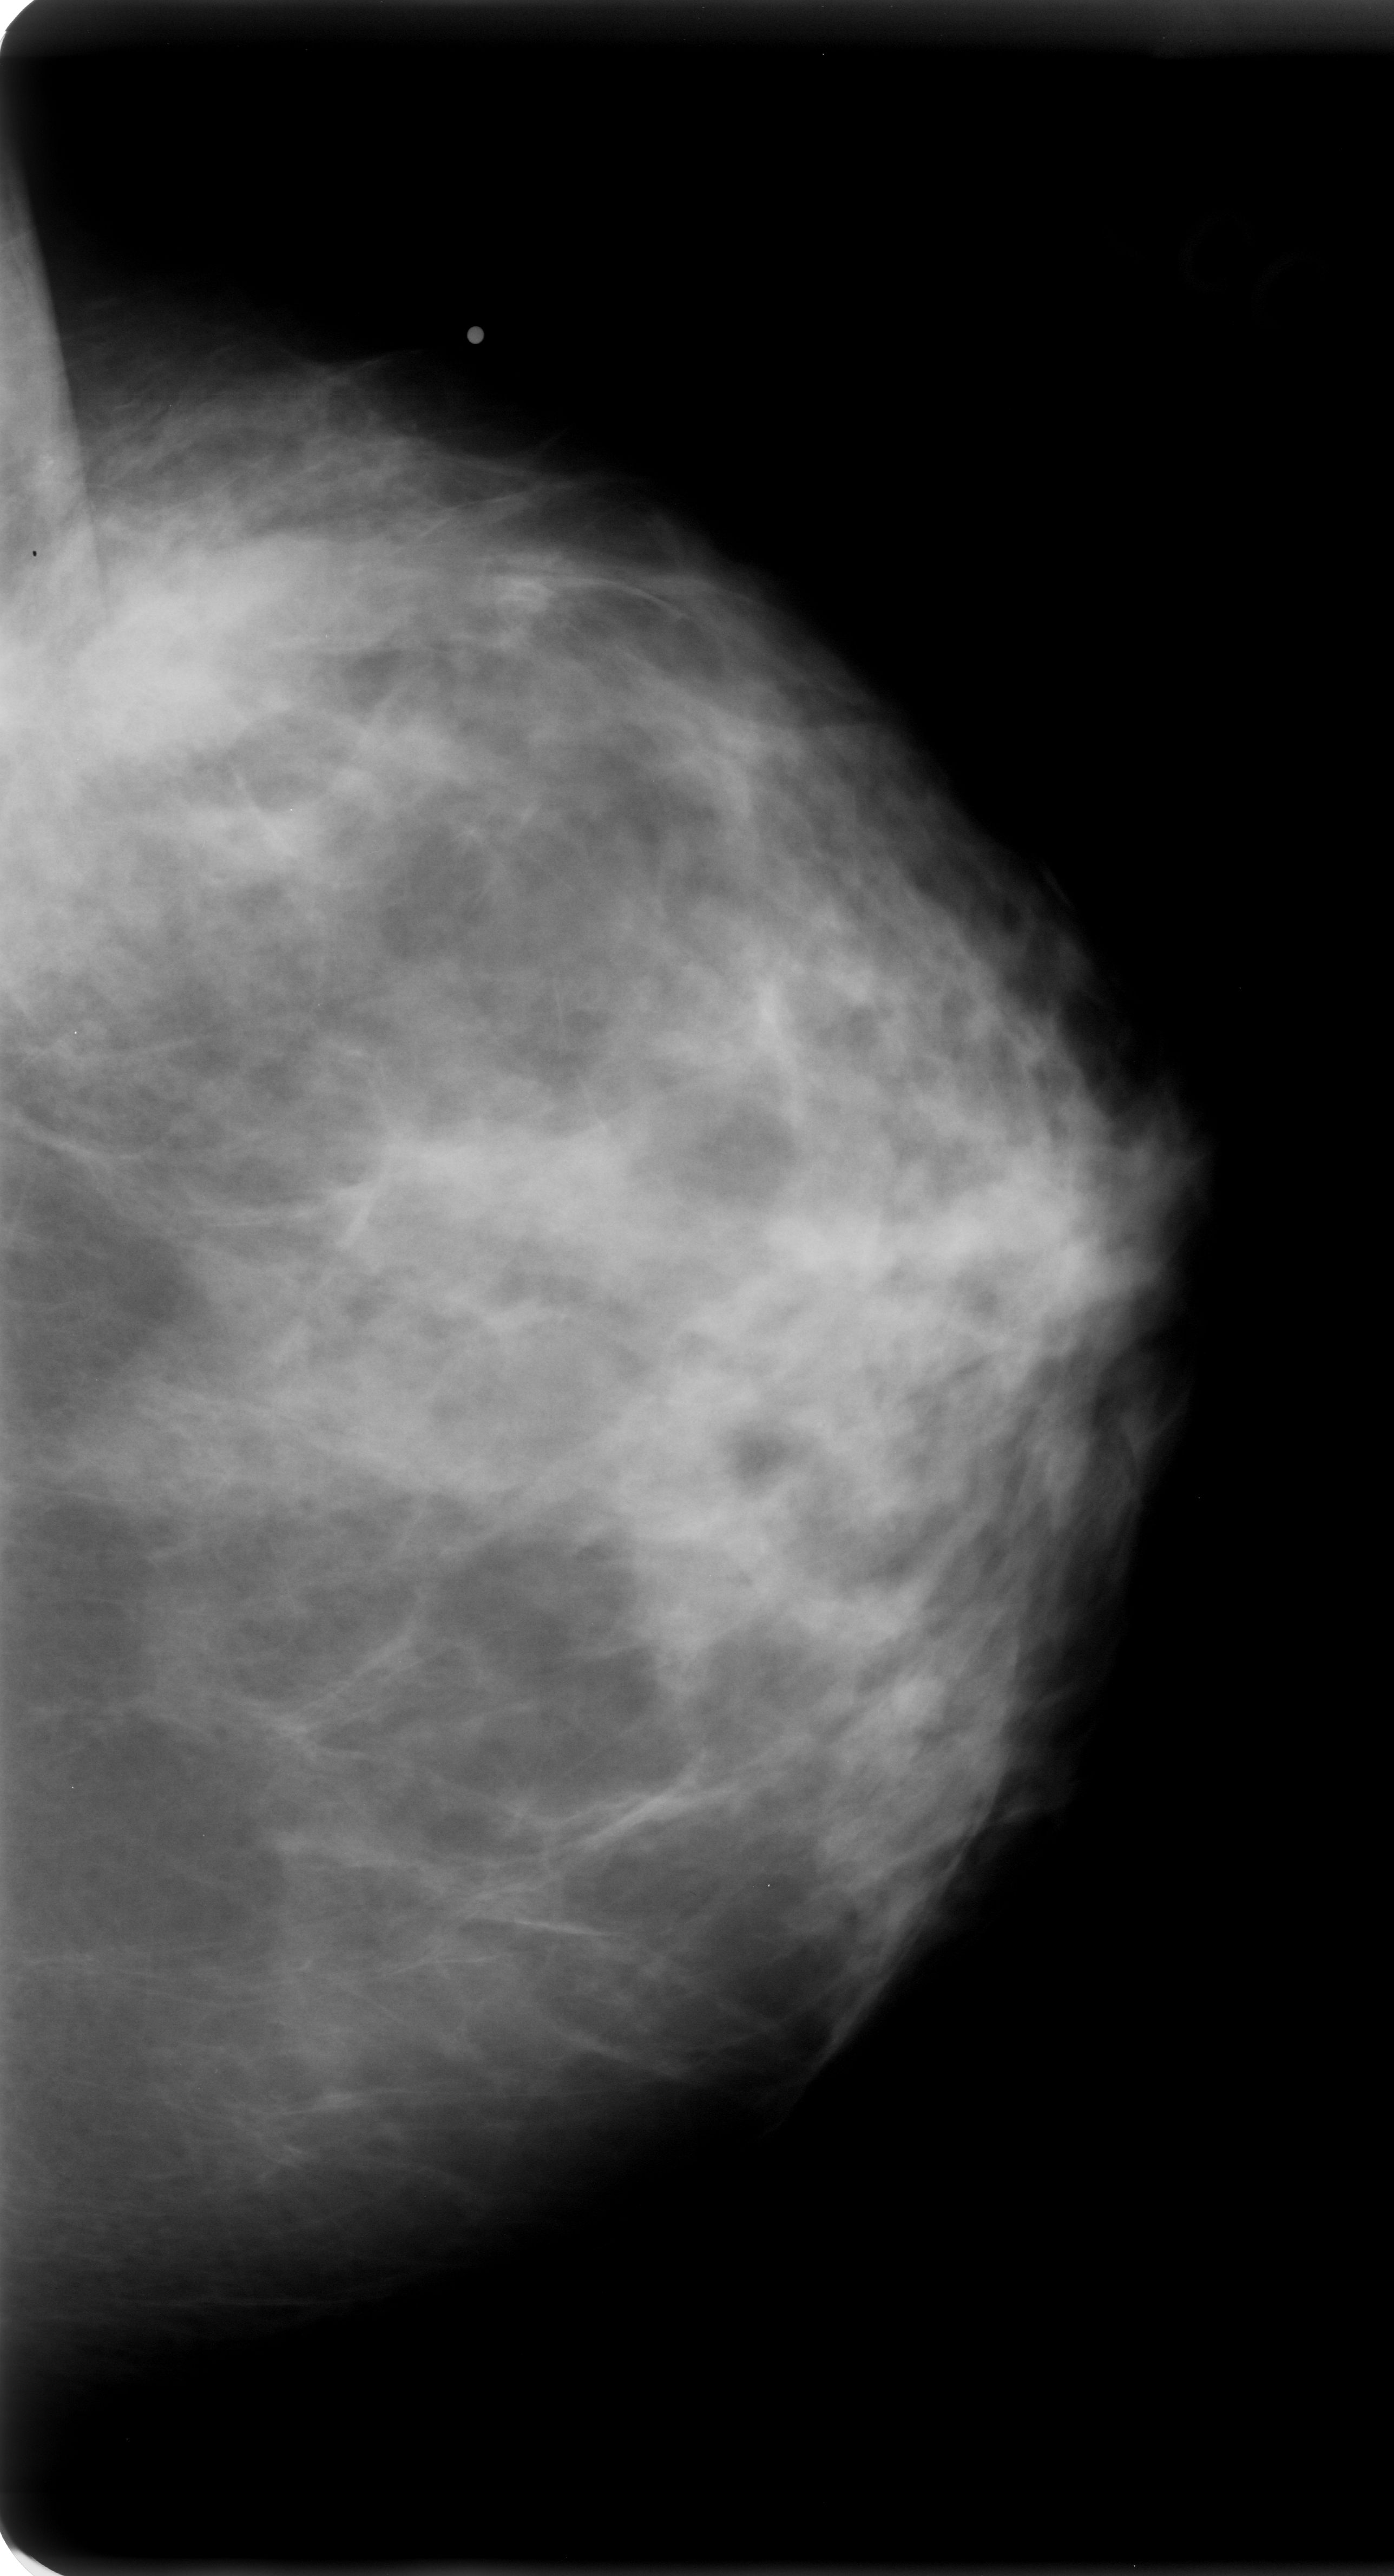
Digitized screen-film mammogram; left breast; CC view; BI-RADS breast density category 3 (scale 1–4); 1394 × 2576 image matrix.
Marked abnormalities (boxes around the expert regions of interest):
- mass, shape irregular, margins ill defined; BI-RADS assessment category 4; subtlety rating 4 on a 1 (subtle) to 5 (obvious) scale; pathology result (as recorded, not read from the image): malignant: bounding box (x1, y1, x2, y2) in pixels: (66, 528, 300, 809)